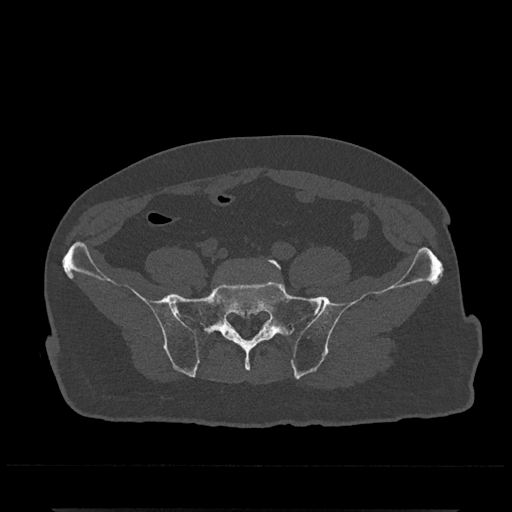
CT including the spine, one axial slice. Bone window (W 1800 / L 400 HU). 512 × 512 image matrix, field of view 393 × 393 mm. Male patient, age 67 years. From the clinical record (not read from this slice): primary cancer: prostate.
Annotated regions visible in this slice (semi-automatic segmentation, software-assisted and operator-edited):
- L5 vertebra: bounding box (x1, y1, x2, y2) in pixels: (268, 258, 281, 269)